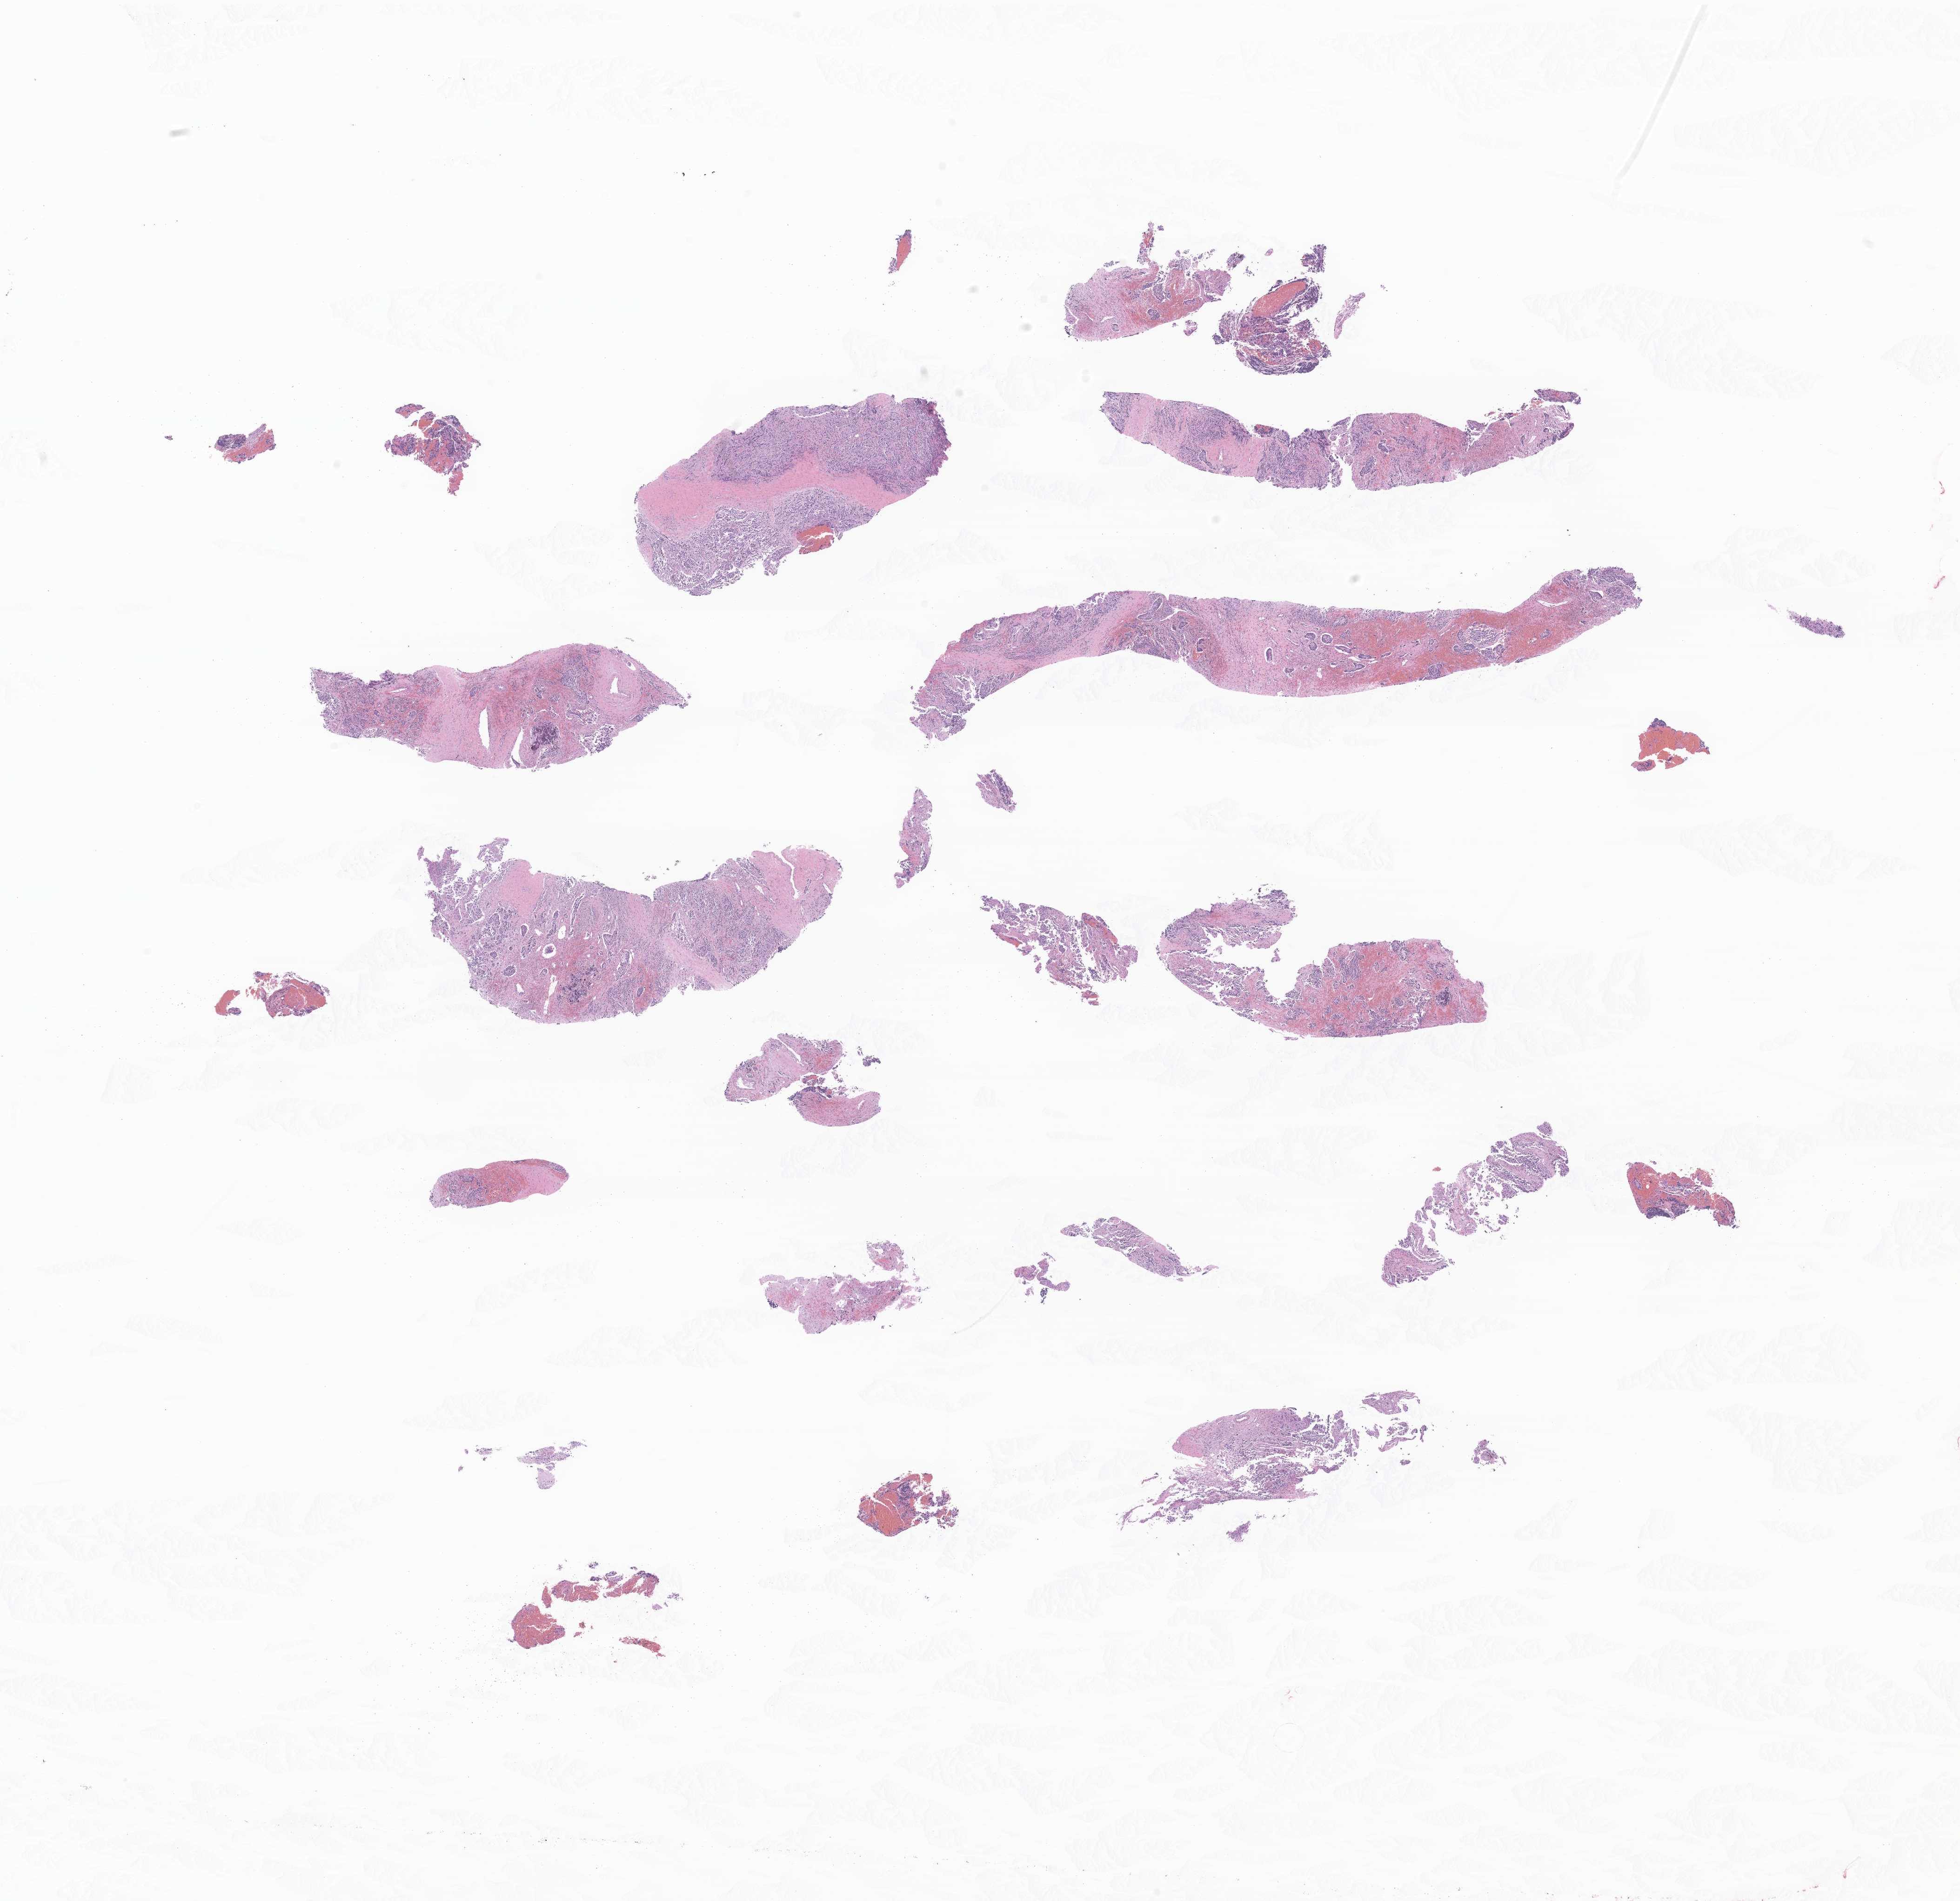
Hematoxylin and eosin (H&E) whole-slide image of tumor tissue from the vertebral column — whole scanned area (about 17.8 x 17.2 mm) shown as a low-resolution overview; formalin-fixed paraffin-embedded section. Patient female; age 495 days (about 1.4 years).
• recorded diagnosis: Neuroblastoma, NOS